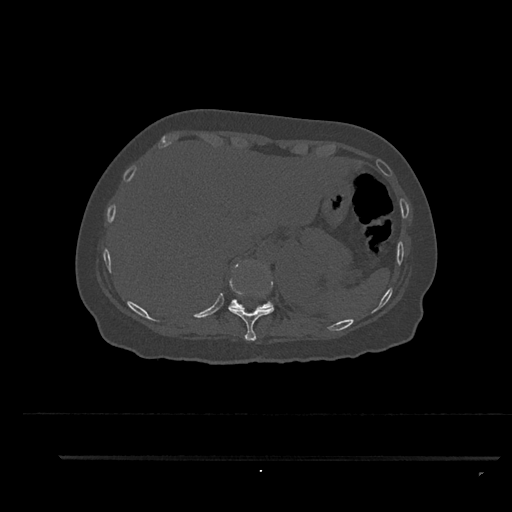
CT including the spine, one axial slice. Position 345 of 797 along the scan axis. Reconstruction kernel Br40s/3. 120 kVp. Bone window (W 1800 / L 400 HU). 0.5 mm slice thickness. 512 × 512 image matrix, field of view 408 × 408 mm. Patient: female, 44 years. From the clinical record (not read from this slice): primary cancer: renal.
Outlined on this slice (semi-automatically segmented with operator editing):
- T10 vertebra: bounding box (x1, y1, x2, y2) in pixels: (228, 289, 274, 341)
- T11 vertebra: (229, 263, 274, 310)